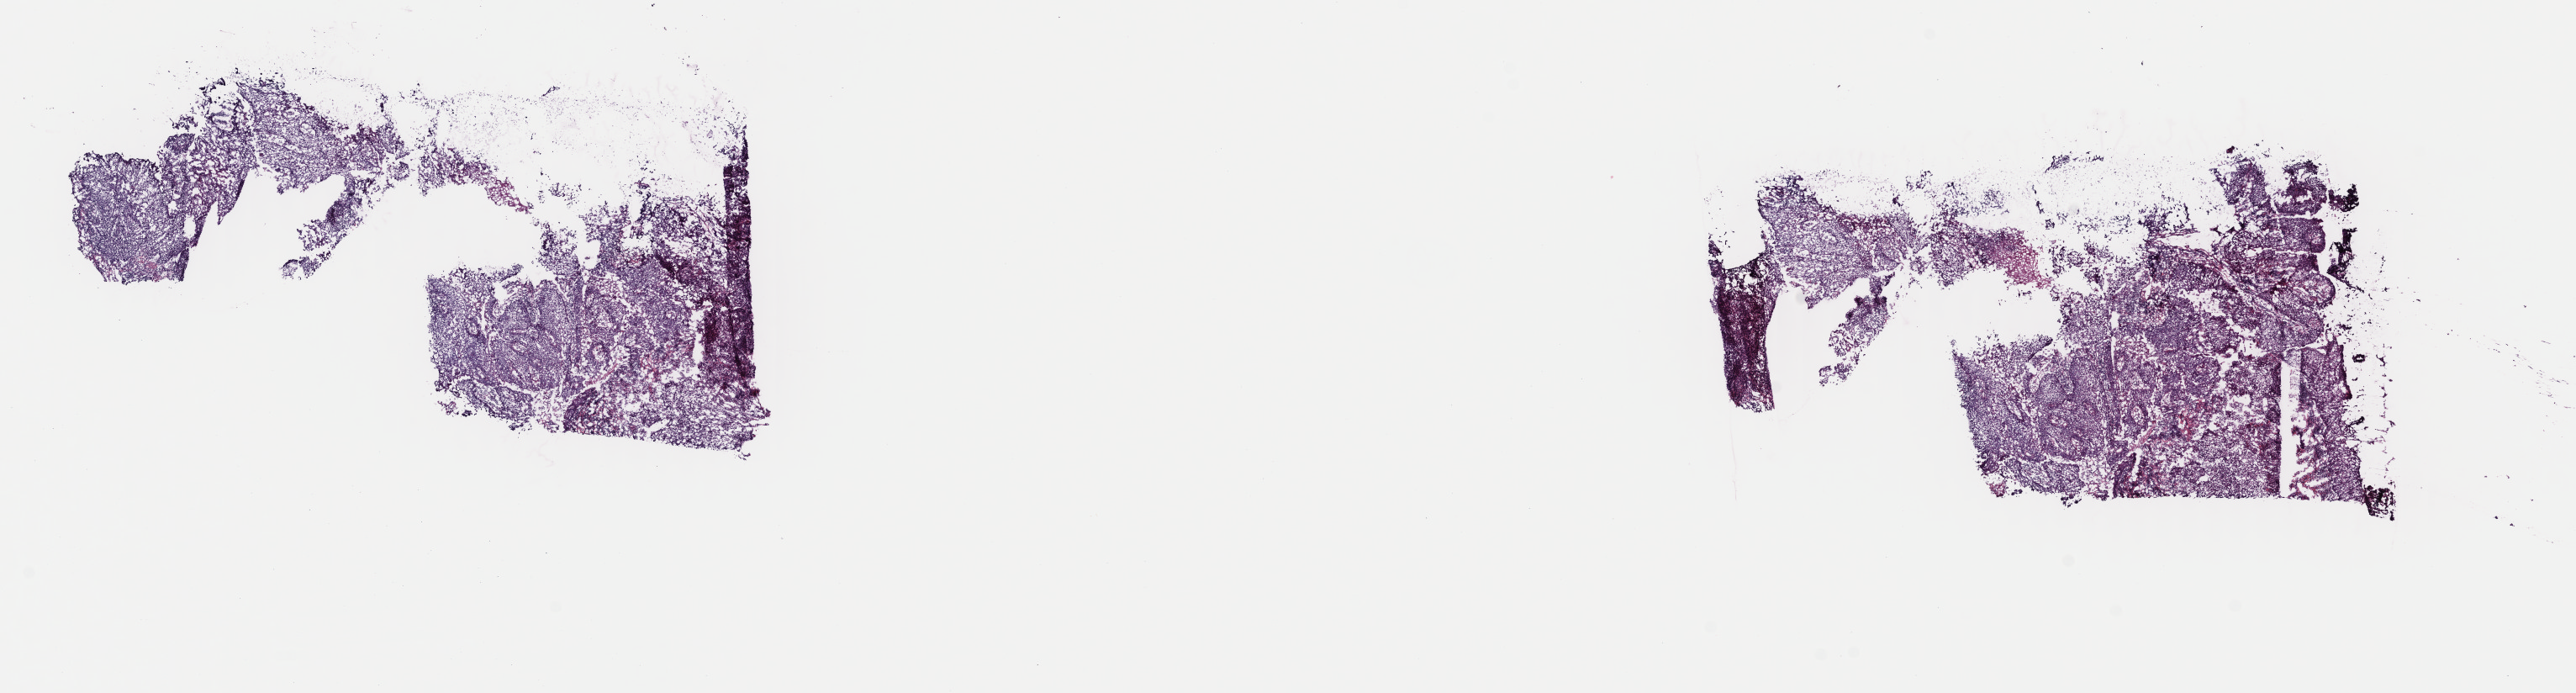
Whole-slide histology image, H&E-stained — shown as a low-resolution overview of the whole scanned area (about 24.2 x 6.5 mm). Frozen section from the top of the tissue portion. Head and neck, primary tumour sample. Female patient; age at initial diagnosis 62 years. Histologic grade: G2 (moderately differentiated). Composition of this section per pathologist review: tumour cells 80%, tumour nuclei 80%, normal cells 0%, stromal cells 20%, necrosis 0%. Inflammatory infiltration, as recorded: lymphocyte infiltration 20%, monocyte infiltration 0%, neutrophil infiltration 0%.
• lymph nodes positive (case pathology): 1 of 67 examined
• laterality: right
• AJCC pathologic stage: IVA (7th edition)
• diagnosis: Squamous cell carcinoma, NOS (hypopharynx, NOS)